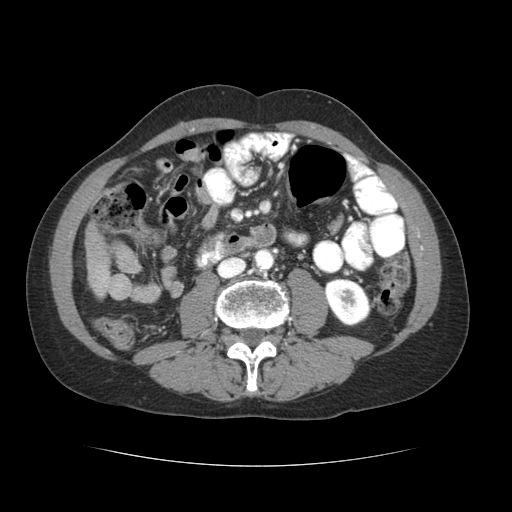
Contrast-enhanced abdominal CT (liver protocol), one axial slice; position 6 of 69 along the scan axis; reconstruction kernel STANDARD; 120 kVp; soft-tissue window (W 400 / L 40 HU); 2.5 mm slice thickness; 512 × 512 image matrix, field of view 360 × 360 mm. From the clinical record (not read from this slice): diagnosis: hepatocellular carcinoma (patient treated with transarterial chemoembolisation; whether this scan precedes or follows treatment is not stated here); TNM stage (as recorded): Stage-II; Child-Pugh class: B; tumour nodularity: multinodular; tumour size: 2.6 cm.
Structures marked on this image (semi-automatically segmented with operator editing):
- liver parenchyma outside the tumour (the mass and vessels are separate outlines, so this box may not span the whole liver): box from (x=84, y=224) to (x=110, y=290) px
- liver vessels: (x=102, y=276)–(x=107, y=283)